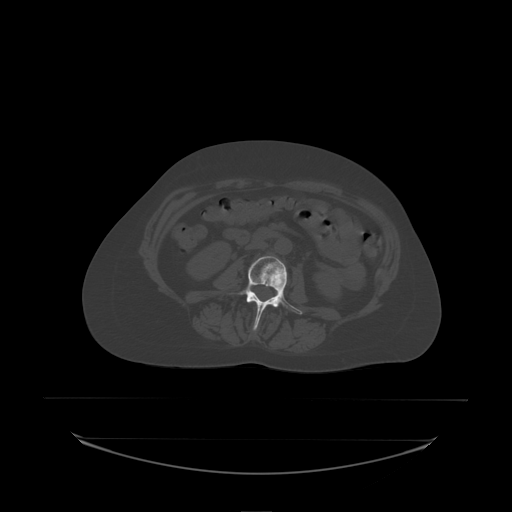
CT including the spine, one axial slice. Slice 61 of 242 in the series (ordered by position). Bone window (W 1800 / L 400 HU). 2.5 mm slice thickness. 512 × 512 image matrix, field of view 500 × 500 mm. Patient: female, 53 years. From the clinical record (not read from this slice): primary cancer: lung; vertebrae with lytic lesions (as recorded): T7, L1.
Outlined on this slice (semi-automatic segmentation, software-assisted and operator-edited):
- L3 vertebra: box from (x=239, y=256) to (x=303, y=331) px